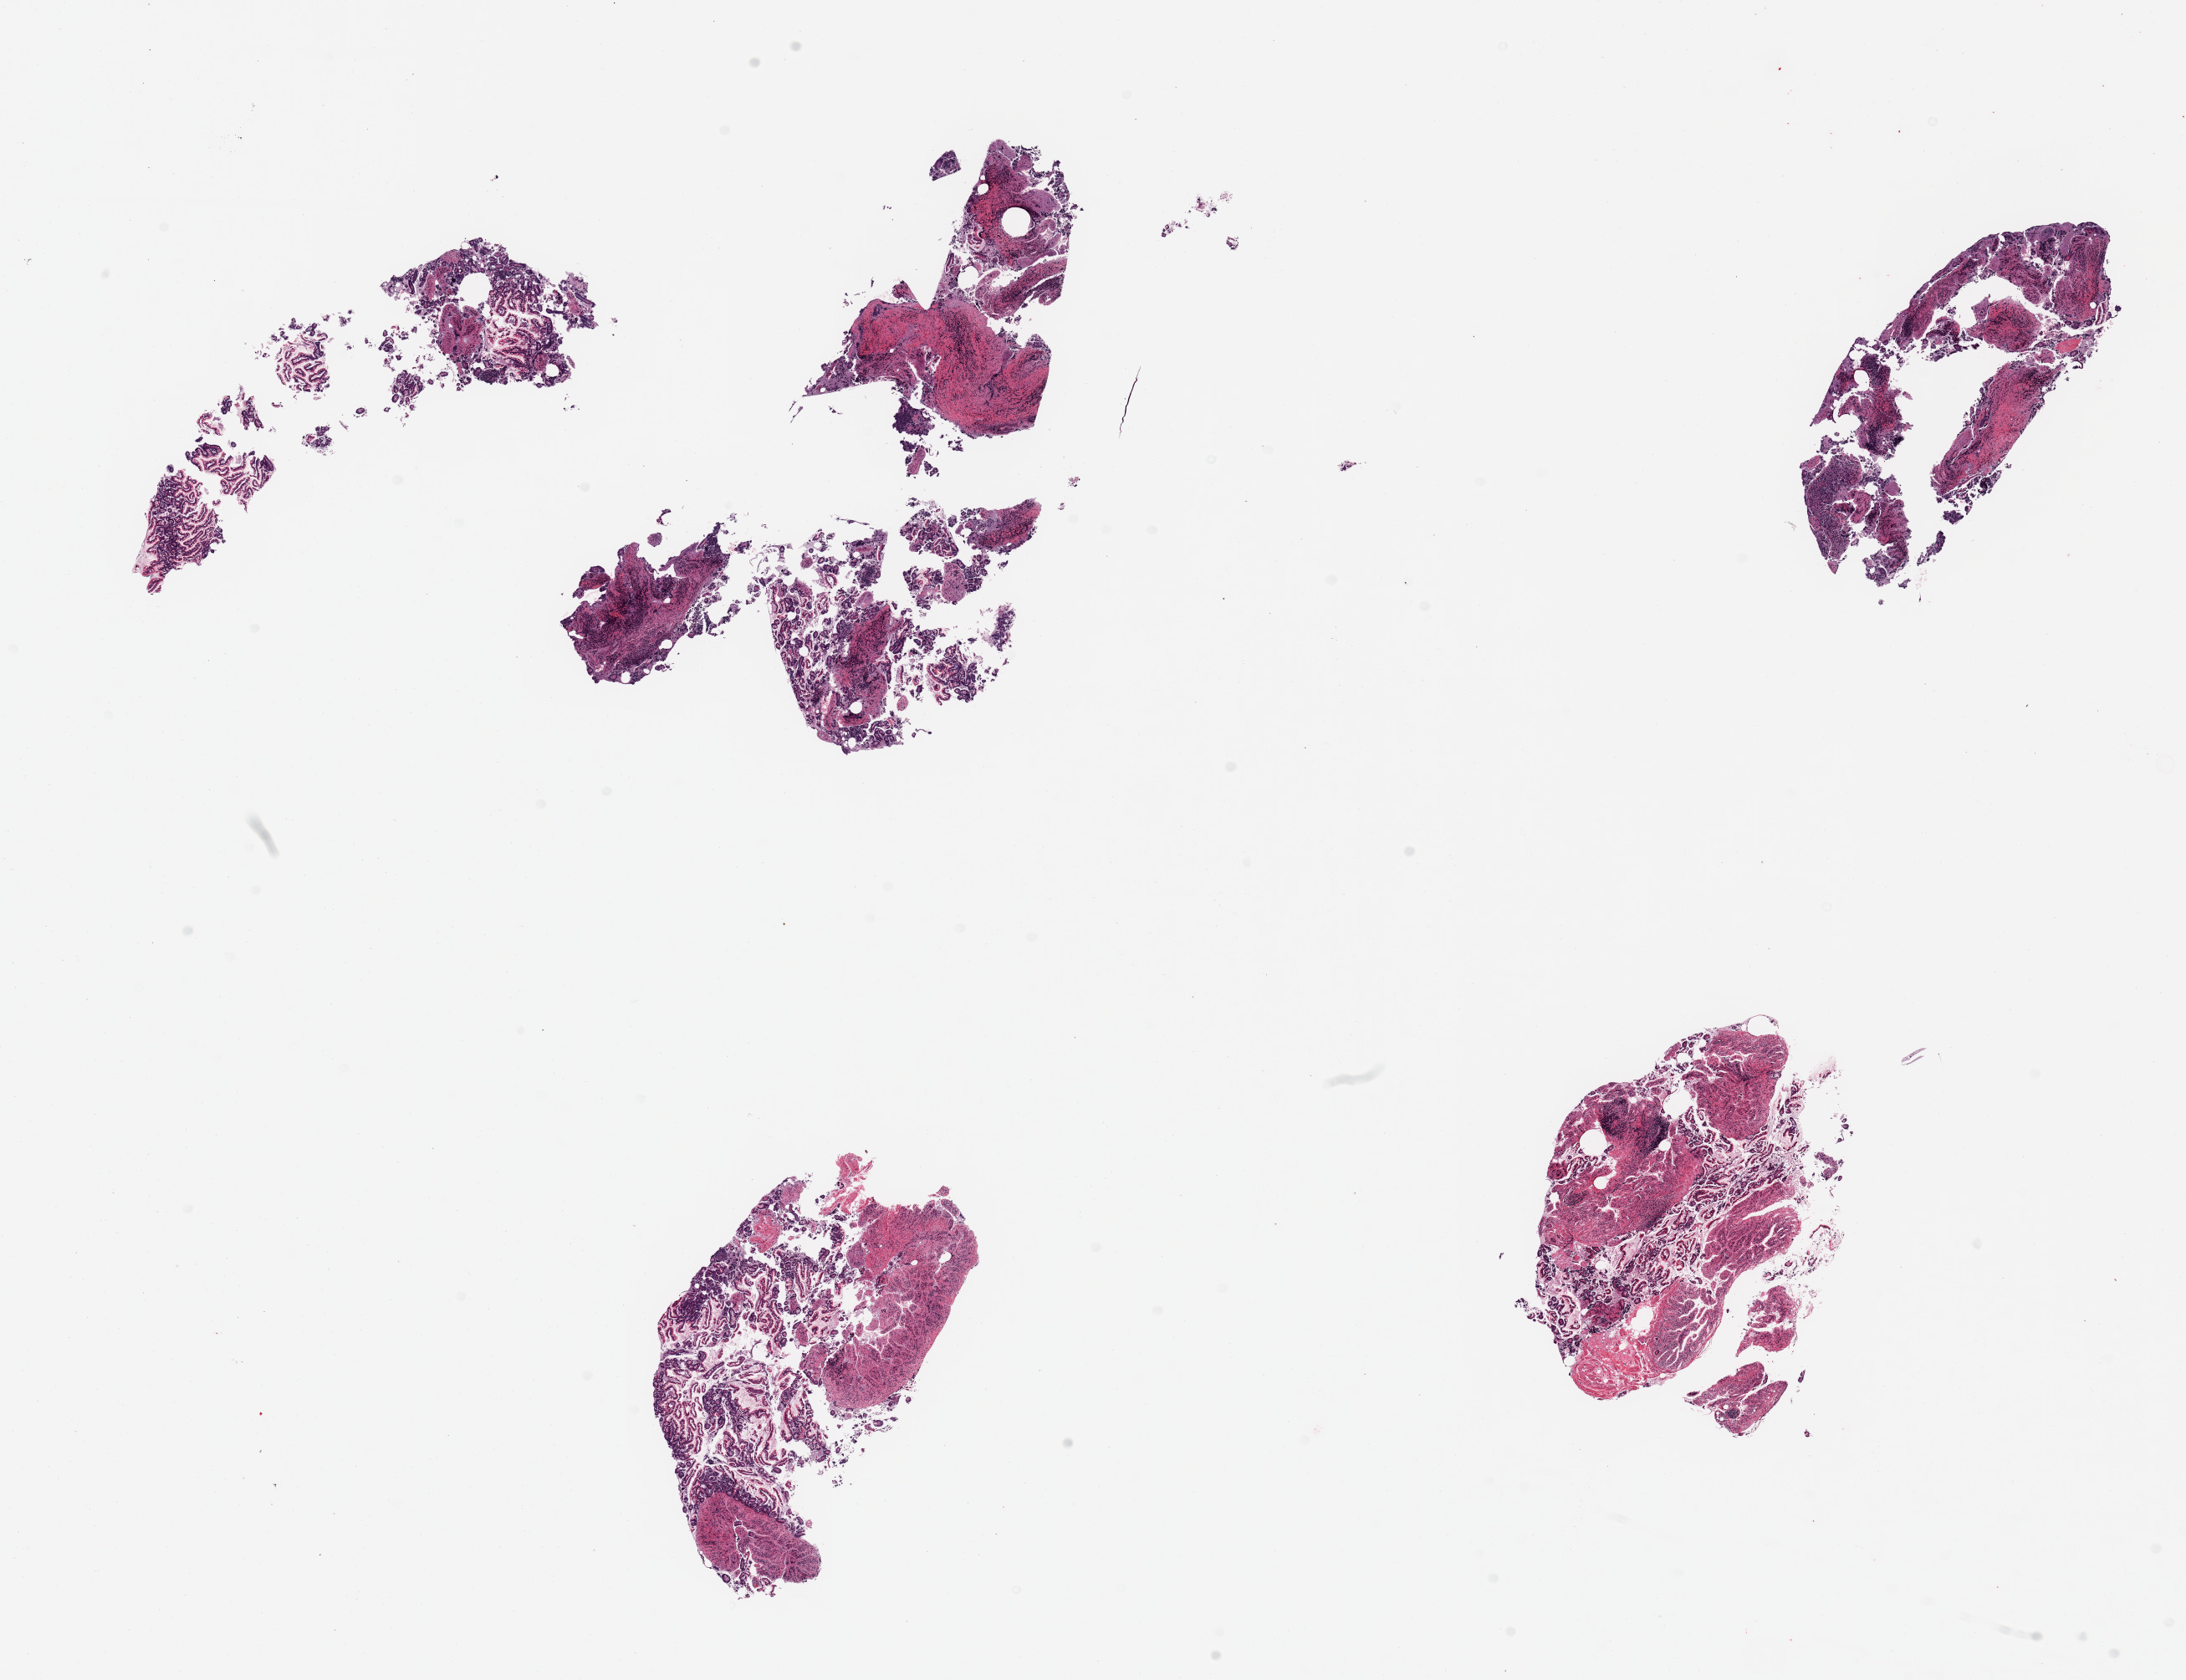
Whole-slide image, haematoxylin and eosin stain — shown as a low-resolution overview of the whole scanned area (about 20.7 x 15.9 mm); PAXgene-fixed paraffin-embedded (PFPE) section; section of ileum (target tissue); tissue donor sample. Donor sex: male.
• reviewer comment on this tissue sample: 4 fragmented pieces; severe autolysis and too little intact lymphoid tissue